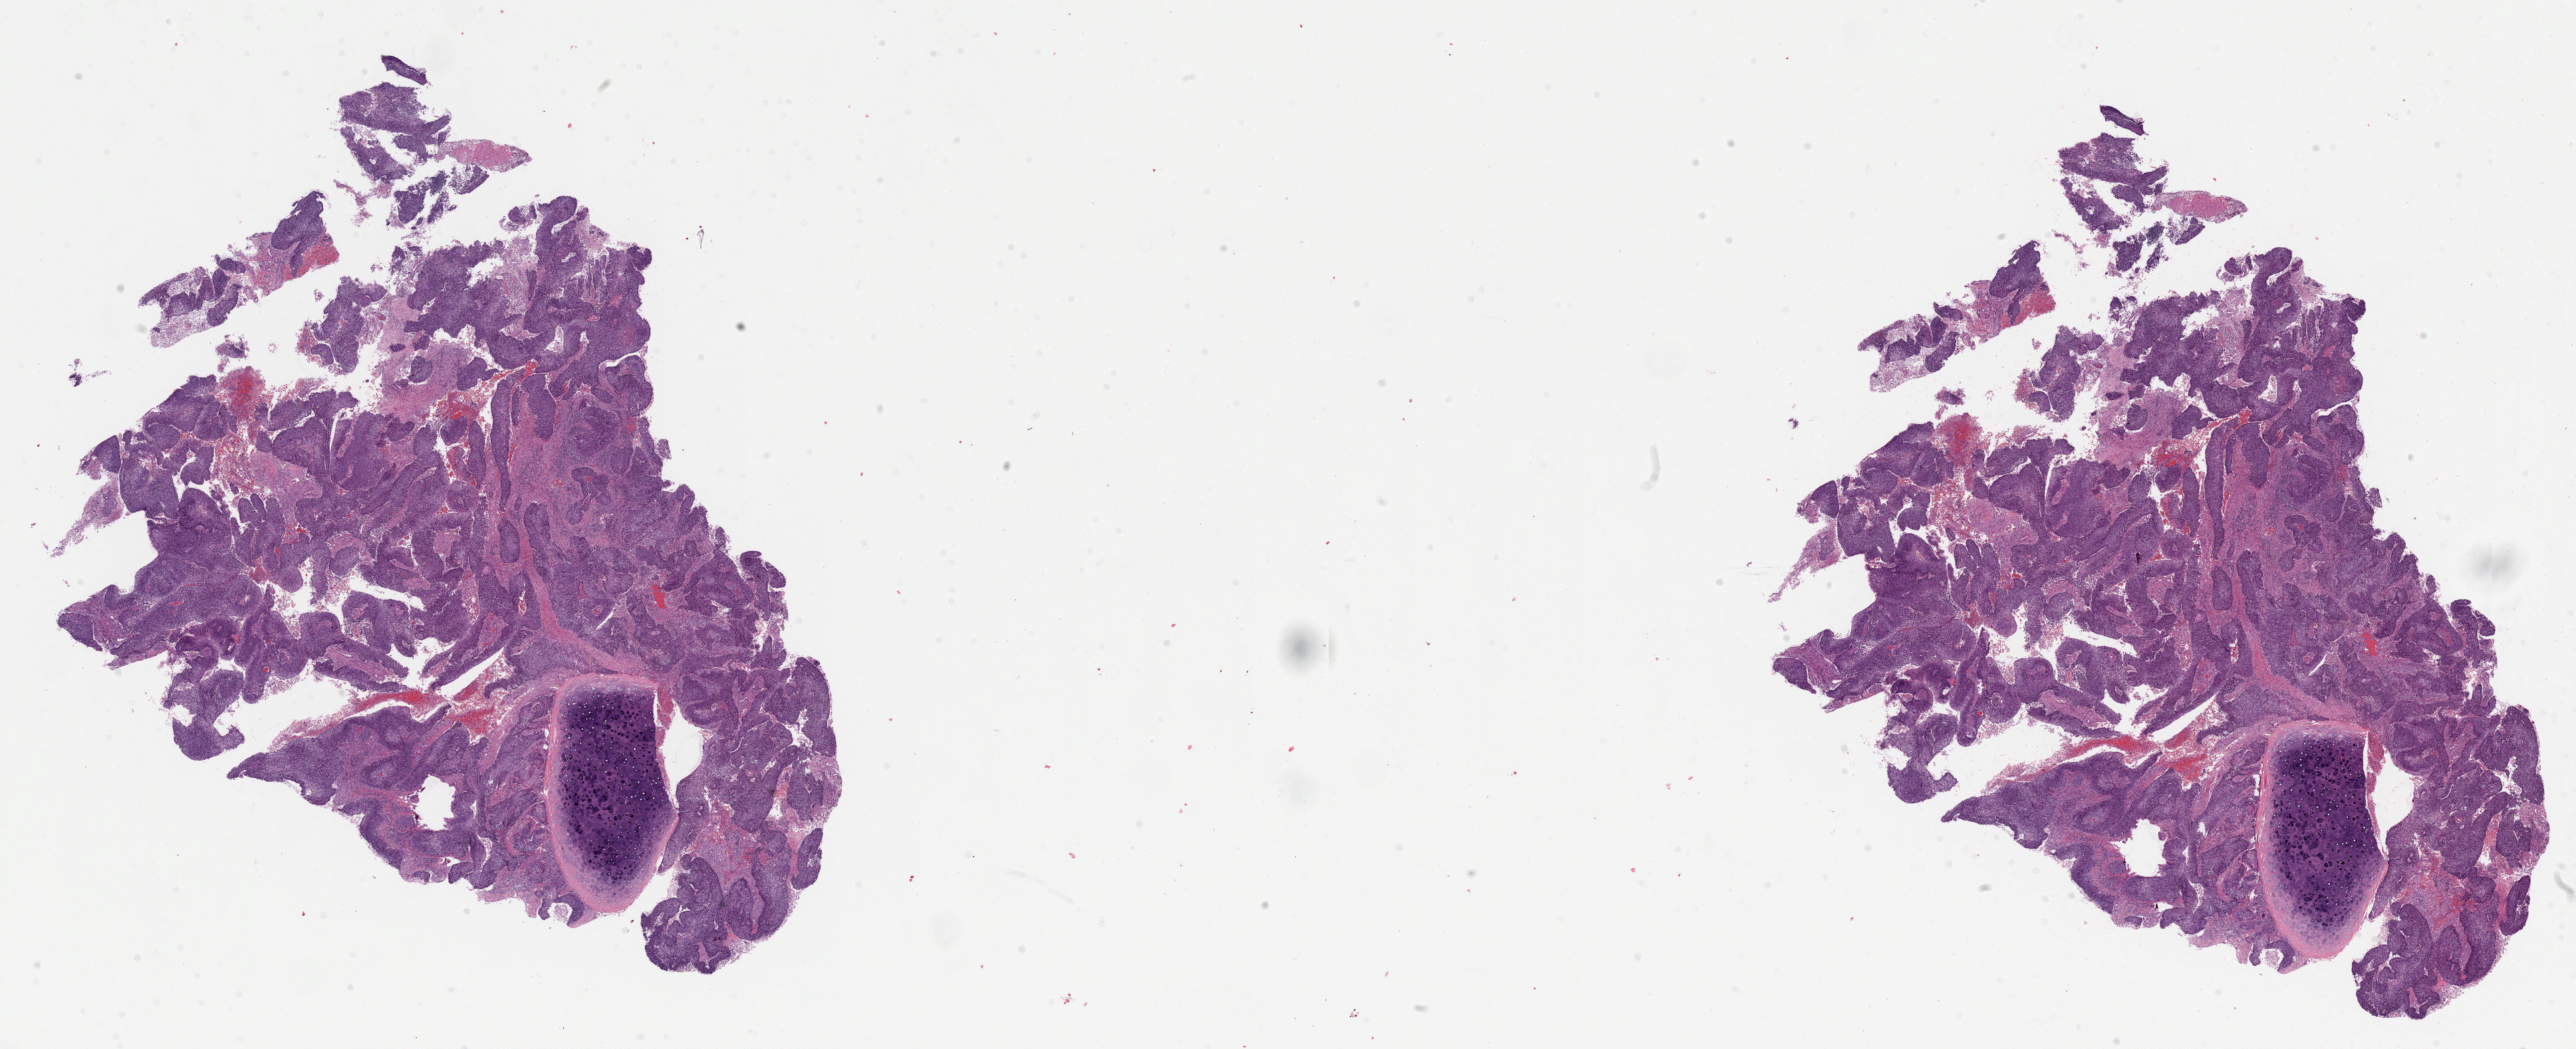
Whole-slide histology image, Hematoxylin and eosin (H&E) stained — low-resolution overview of the scanned area, about 31.0 x 12.6 mm (from a 20x scan), formalin-fixed paraffin-embedded (FFPE) diagnostic section, primary tumour sample from the lung. Male patient; age at initial diagnosis 48 years.
AJCC pathologic stage: IIB. Pathologic diagnosis: Squamous cell carcinoma, NOS (lower lobe, lung).